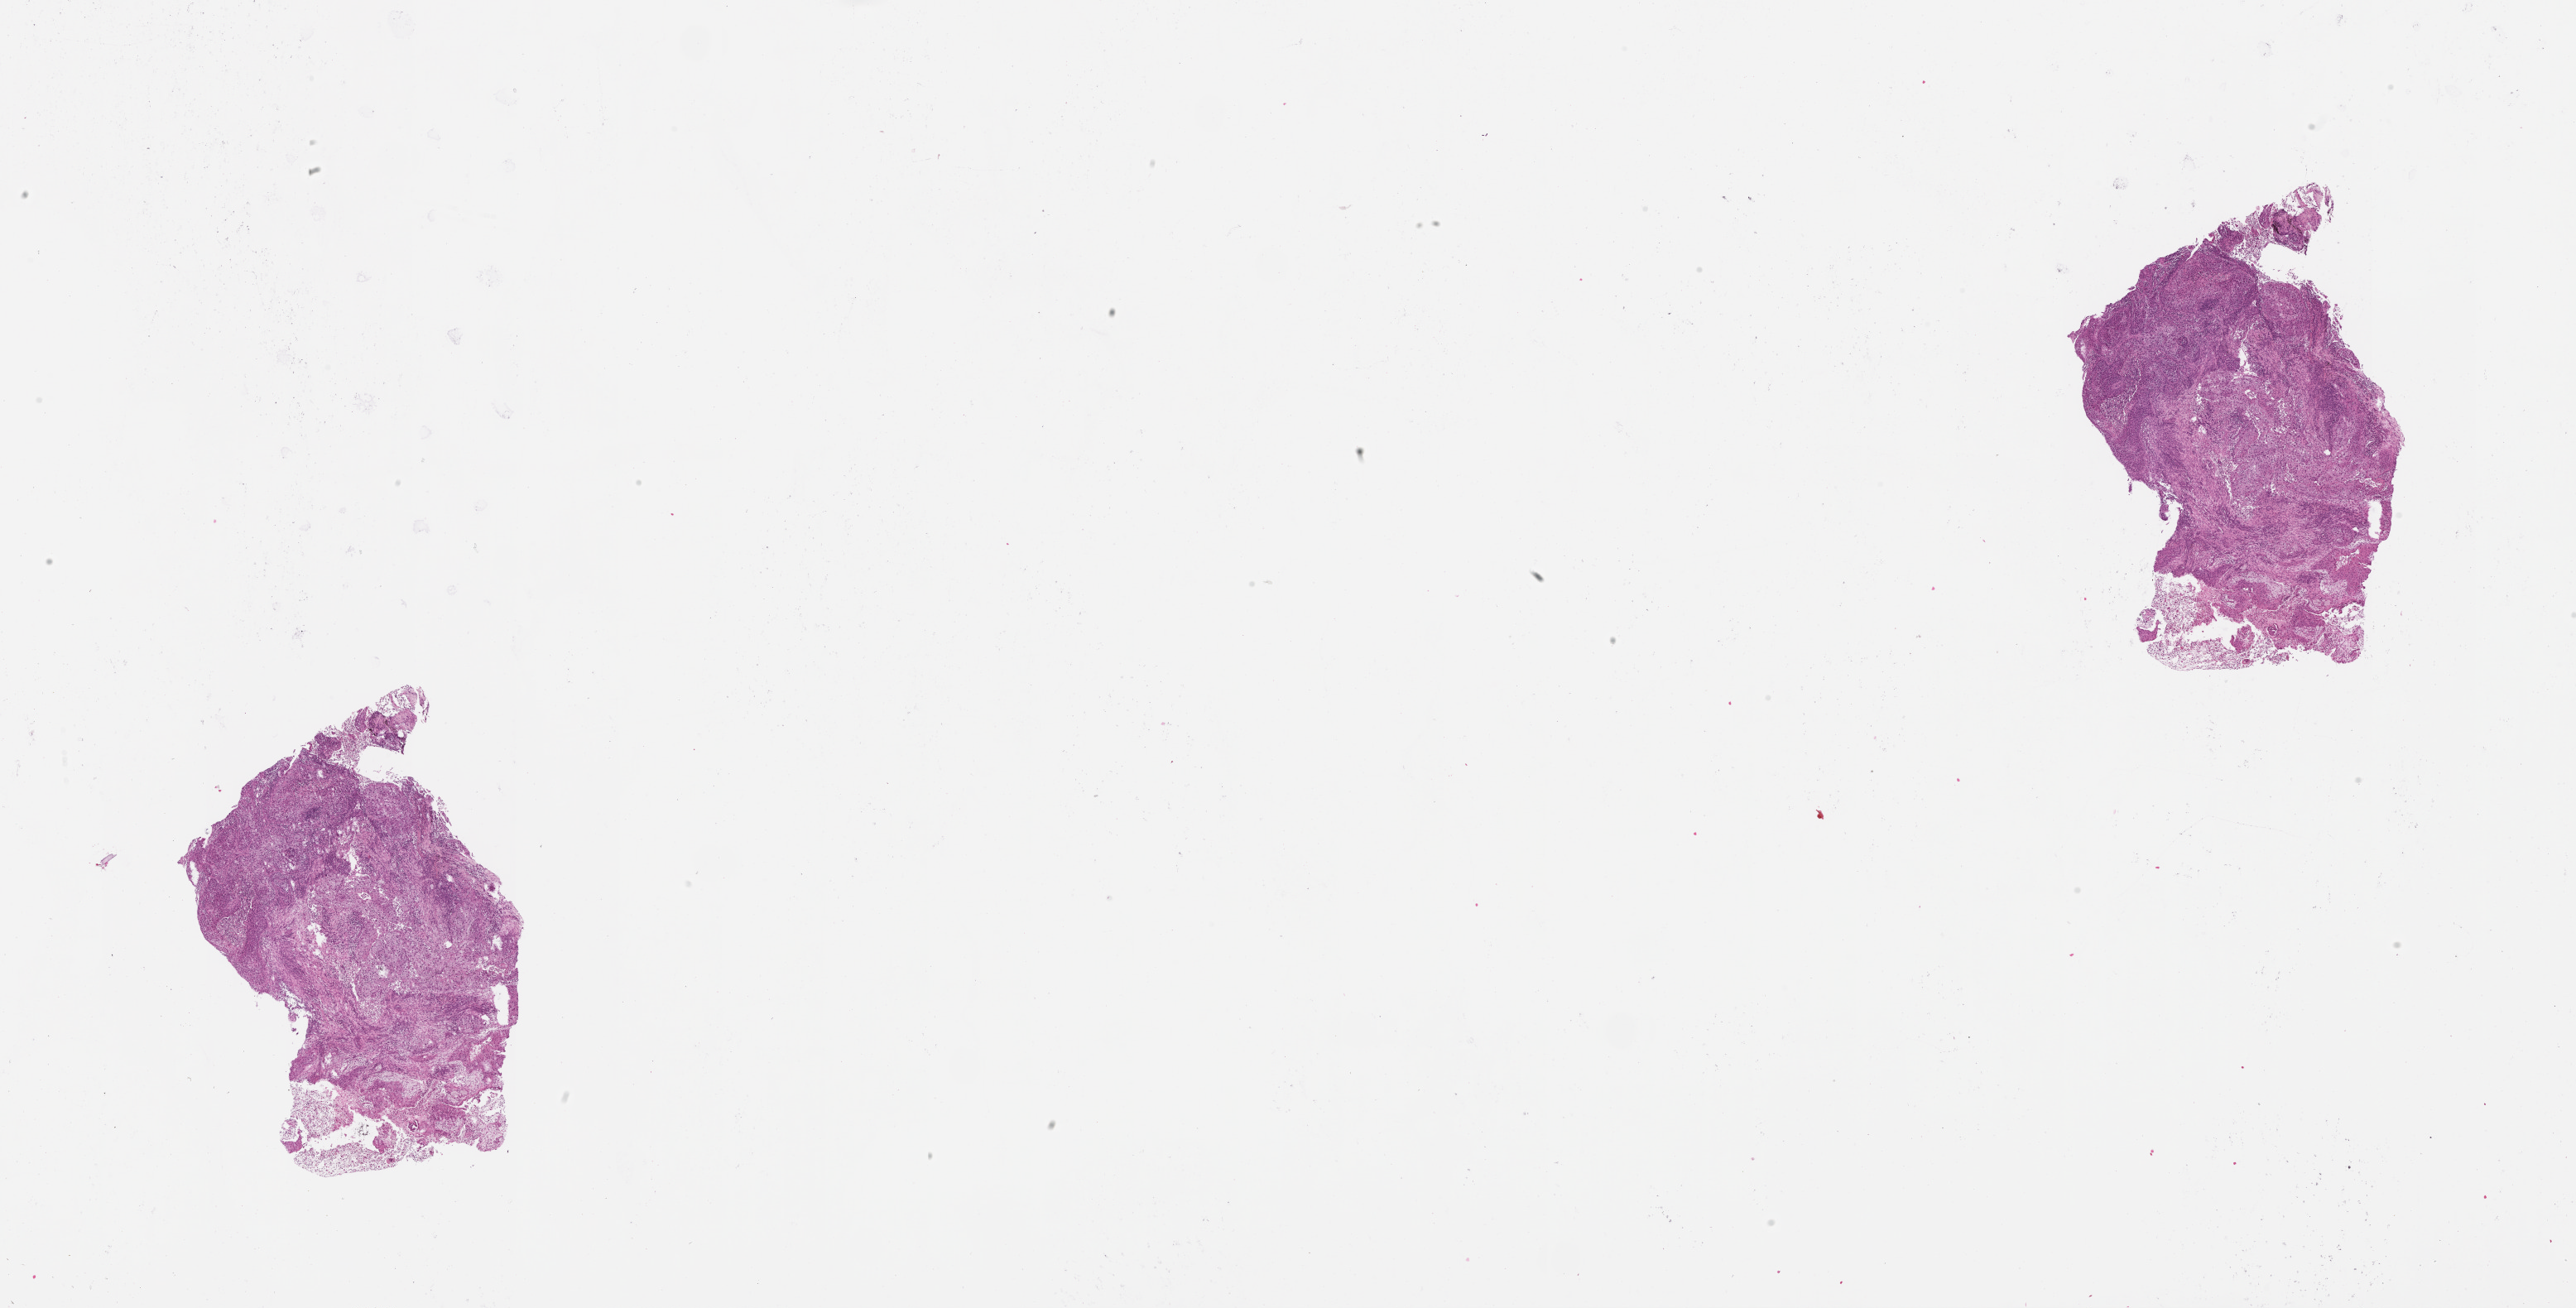
Digitized Hematoxylin and eosin (H&E) stained tissue section (whole slide), whole scanned area (about 25.1 x 12.7 mm) shown as a low-resolution overview, lung, tumour tissue. Male, 60 y/o.
Patient diagnosis (cohort enrolment): squamous cell carcinoma (lung).